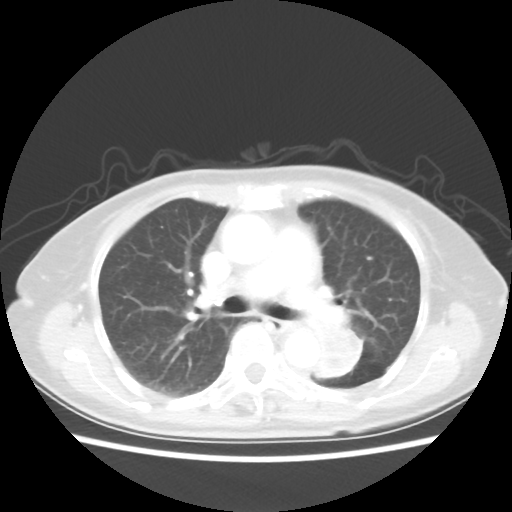
Chest CT, one axial slice; position 31 of 50 along the scan axis; 80 kVp; lung window (W 1500 / L -600 HU); 5 mm slice thickness; 512 × 512 image matrix, field of view 335 × 335 mm. Patient: female, 81 years. Case-level facts recorded for this patient, not image findings: clinical TNM (as recorded): T2 N0 M1a.
Annotated regions visible in this slice (rectangle marked by the reading radiologist):
- lung tumour (recorded histology: squamous cell carcinoma): bounding box [x1, y1, x2, y2] px = [304, 311, 367, 385]